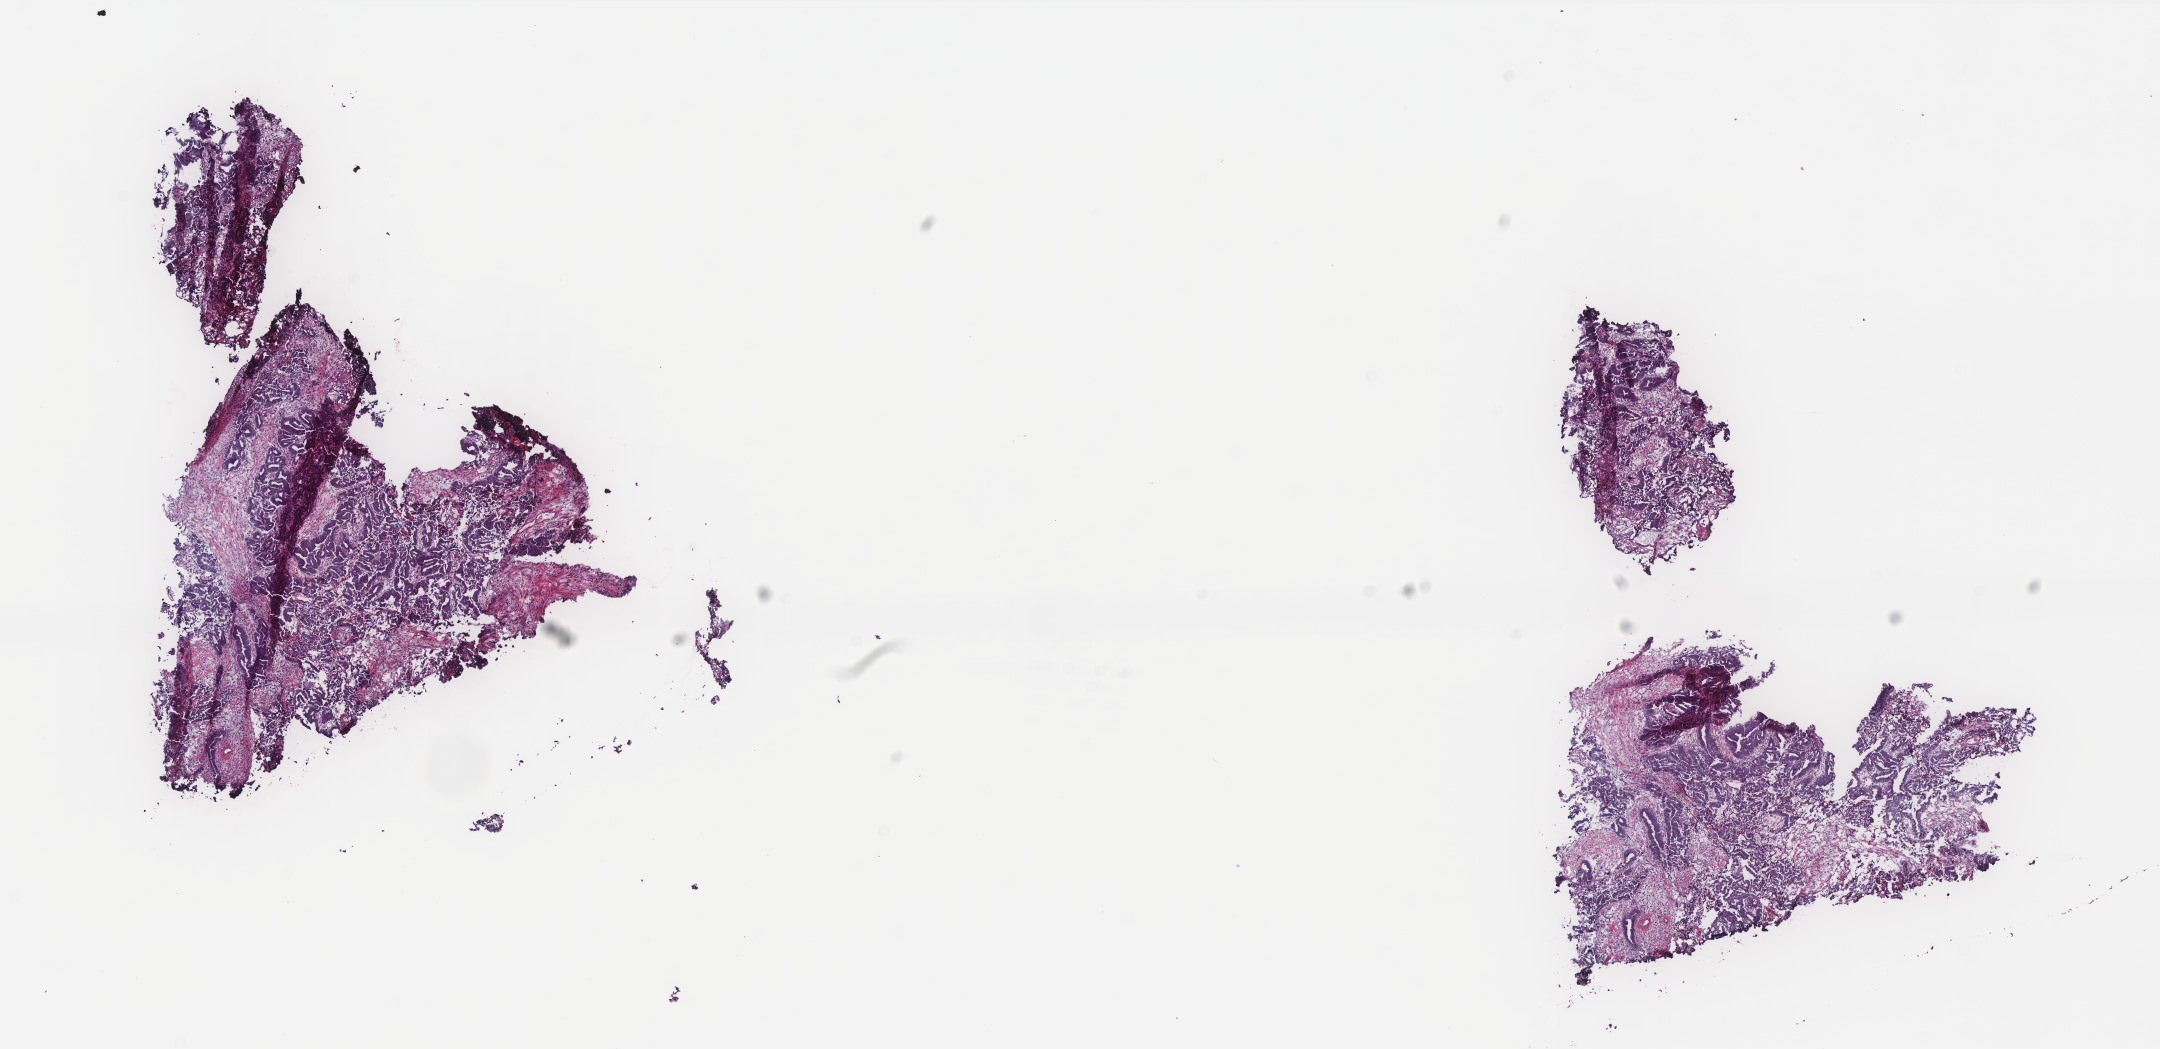
H&E-stained whole-slide image — whole scanned area (about 17.3 x 8.4 mm, from a 40x scan) shown as a low-resolution overview, frozen section, sample: primary tumour, cervix. Patient: female, age at initial diagnosis 61 years. Histologic grade: G2 (moderately differentiated). Slide review estimates, as recorded: tumour cells 70%, tumour nuclei 70%, normal cells 0%, stromal cells 20%, necrosis 10%. Infiltration values recorded for this section: lymphocyte infiltration 40%, monocyte infiltration 20%, neutrophil infiltration 20%.
- histologic diagnosis: Adenocarcinoma, NOS (cervix uteri)
- lymph nodes positive (case pathology): 0 of 18 examined
- FIGO stage: IB1